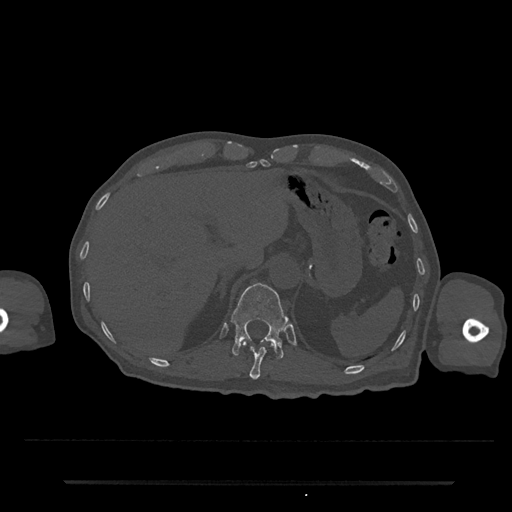
CT including the spine, one axial slice. Position 219 of 797 along the scan axis. Reconstruction kernel Br40s/3. 120 kVp. Bone window (W 1800 / L 400 HU). 0.5 mm slice thickness. 512 × 512 image matrix, field of view 427 × 427 mm. Male patient, age 74 years. From the clinical record (not read from this slice): primary cancer: prostate.
Outlined on this slice (semi-automatically segmented with operator editing):
- T11 vertebra: box from (x=241, y=340) to (x=274, y=380) px
- T12 vertebra: (x=231, y=283)–(x=289, y=359)